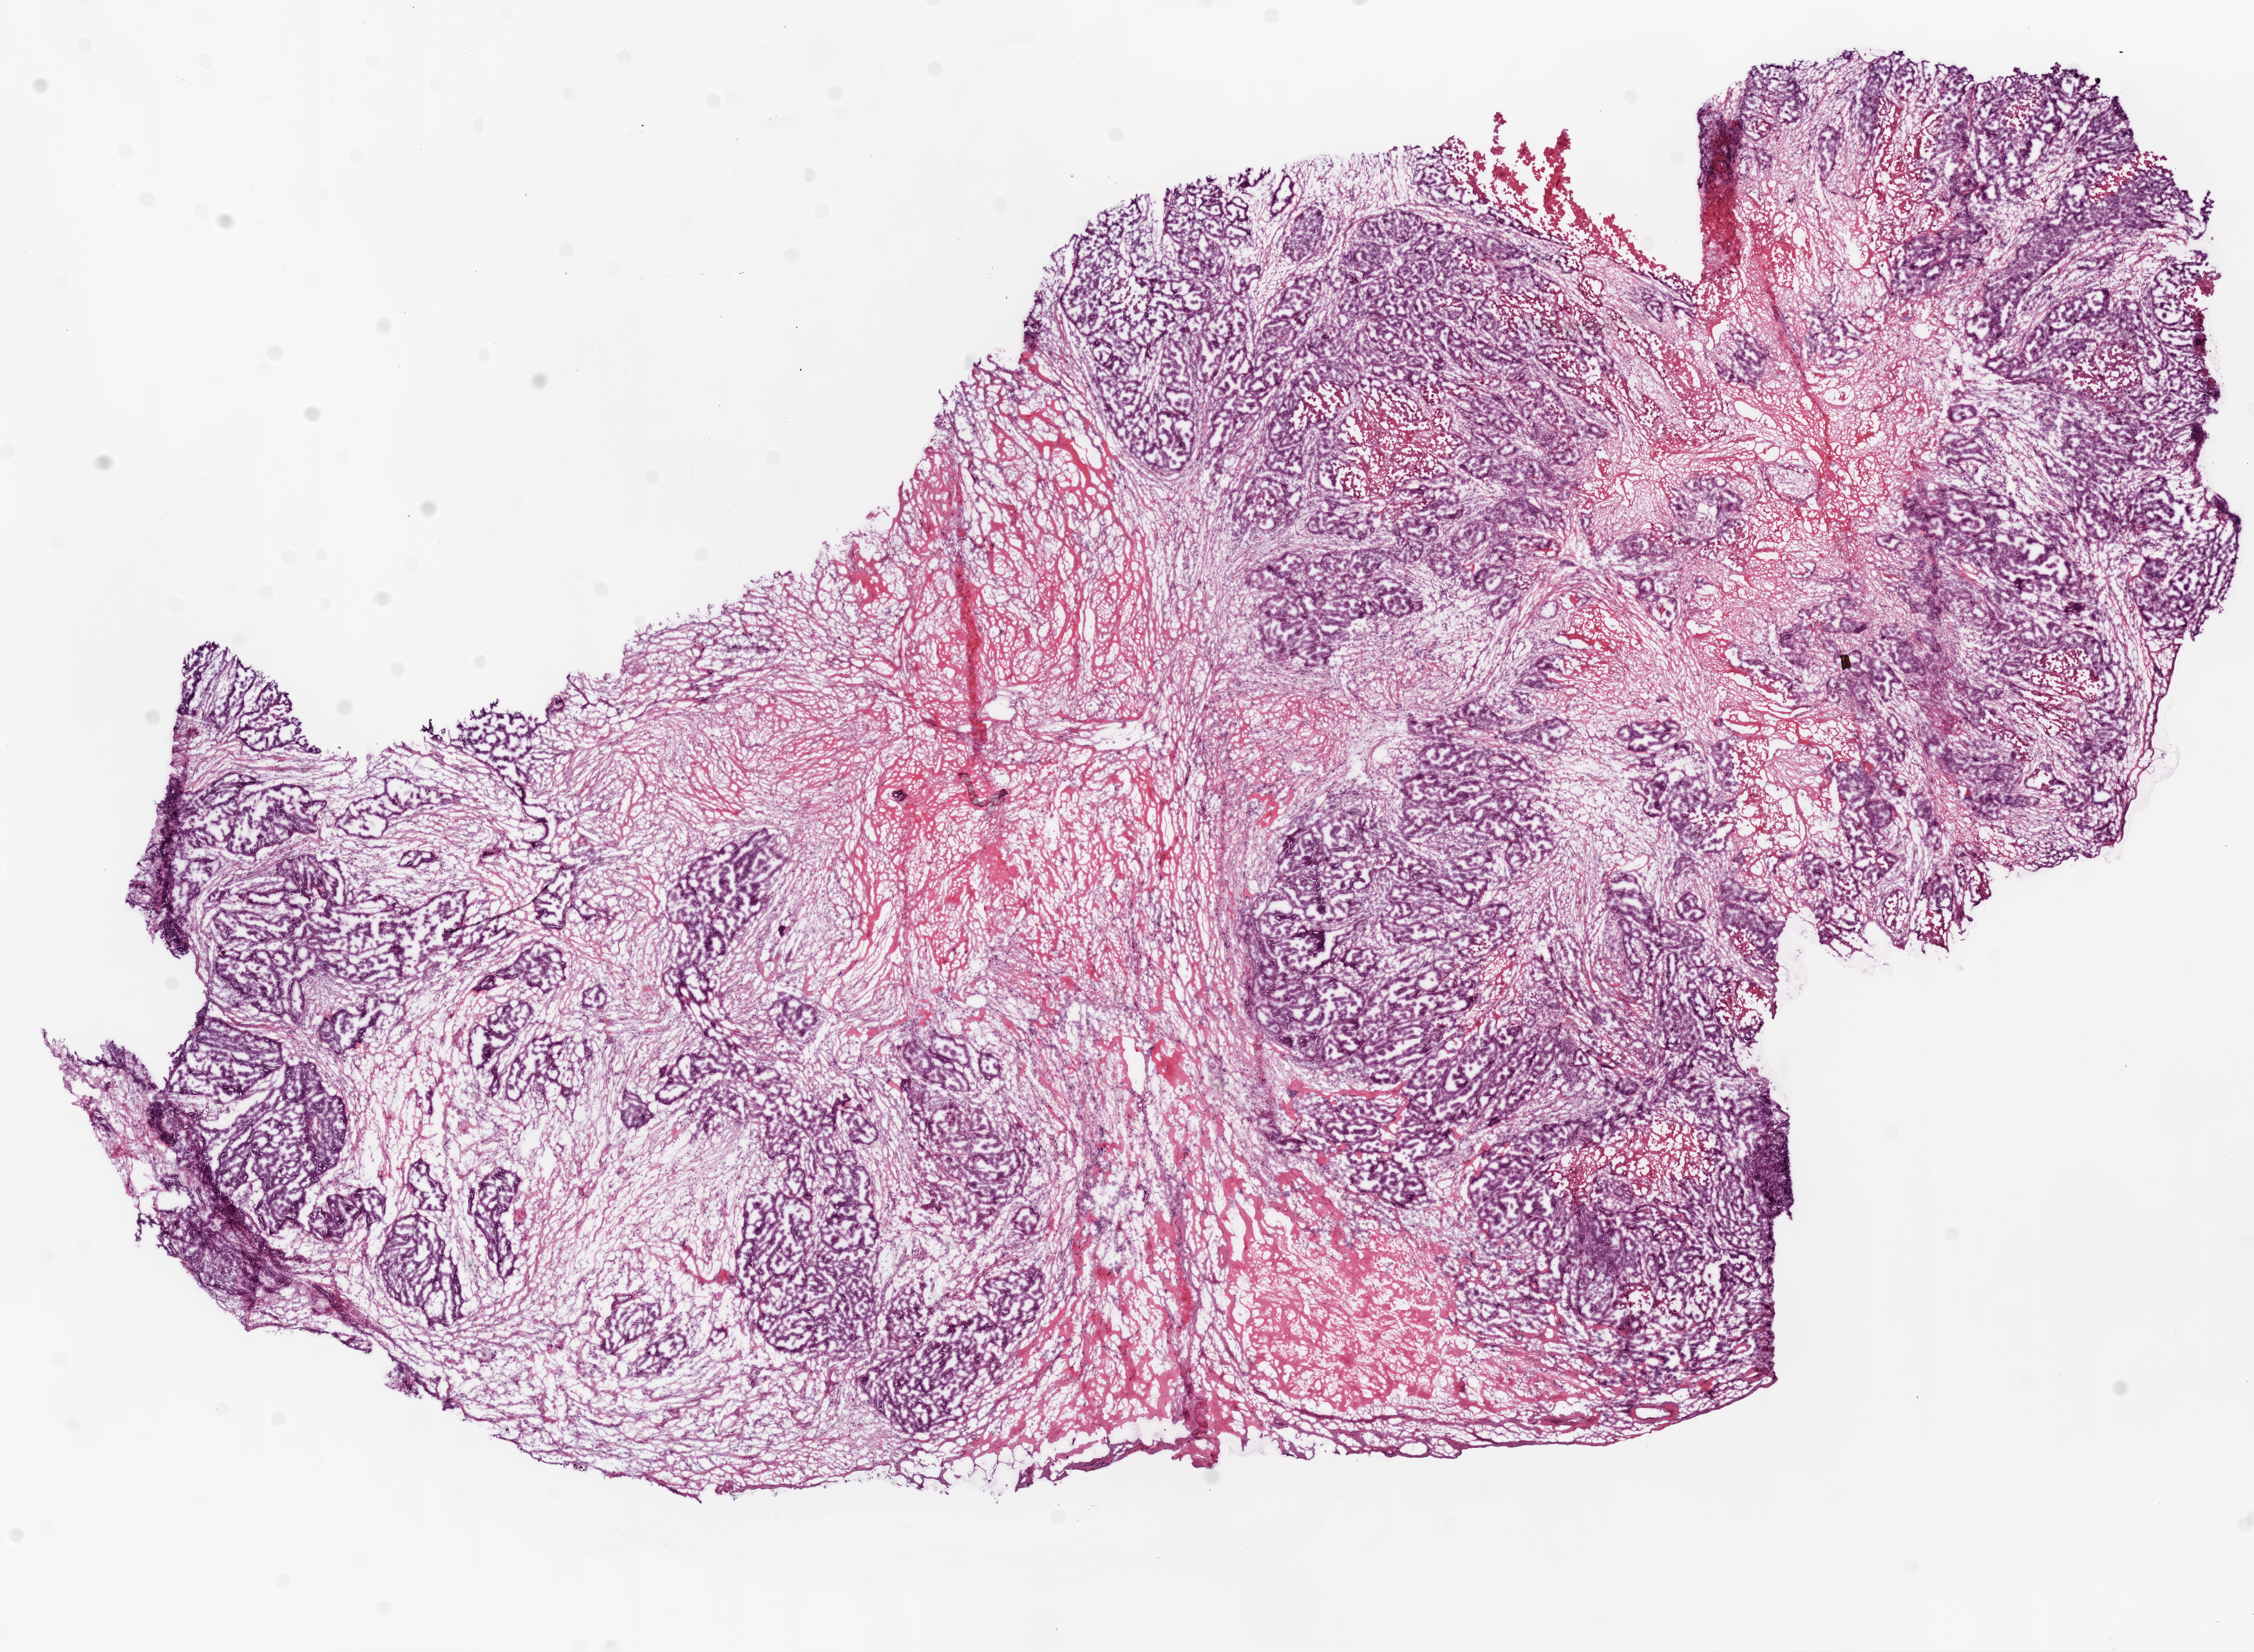
Whole-slide histology image, H&E-stained, low-resolution overview of the scanned area, about 14.0 x 10.3 mm, frozen section from the bottom of the tissue portion, ovary, primary tumour sample. Female patient; age at initial diagnosis 68 years.
Diagnosis: Serous cystadenocarcinoma, NOS.